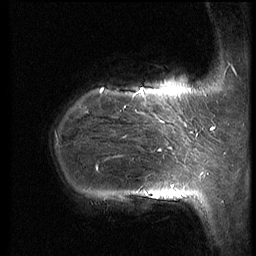
Breast MRI (dynamic contrast-enhanced), one sagittal slice; position 17 of 66 along the scan axis; dynamic contrast-enhanced series, image 2 of 3 at this slice position (ordered by acquisition); 1.5 T; TE 4.2 ms, TR 8.9 ms; 2.5 mm slice thickness; 256 × 256 image matrix, field of view 200 × 200 mm. Patient: female, 39 years. Case-level facts recorded for this patient, not image findings: setting: breast cancer imaged before/during neoadjuvant chemotherapy; receptor status: HER2-positive.
Outlined on this slice (semi-automatic segmentation, software-assisted and operator-edited):
- analysis volume of interest (the breast-tissue region the enhancement analysis was run in; not a lesion): bounding box <48,75,188,218> (left, top, right, bottom; pixels)
- tumour enhancement mask (voxels above the 140 % enhancement threshold inside the analysis volume of interest): <97,89,186,201>